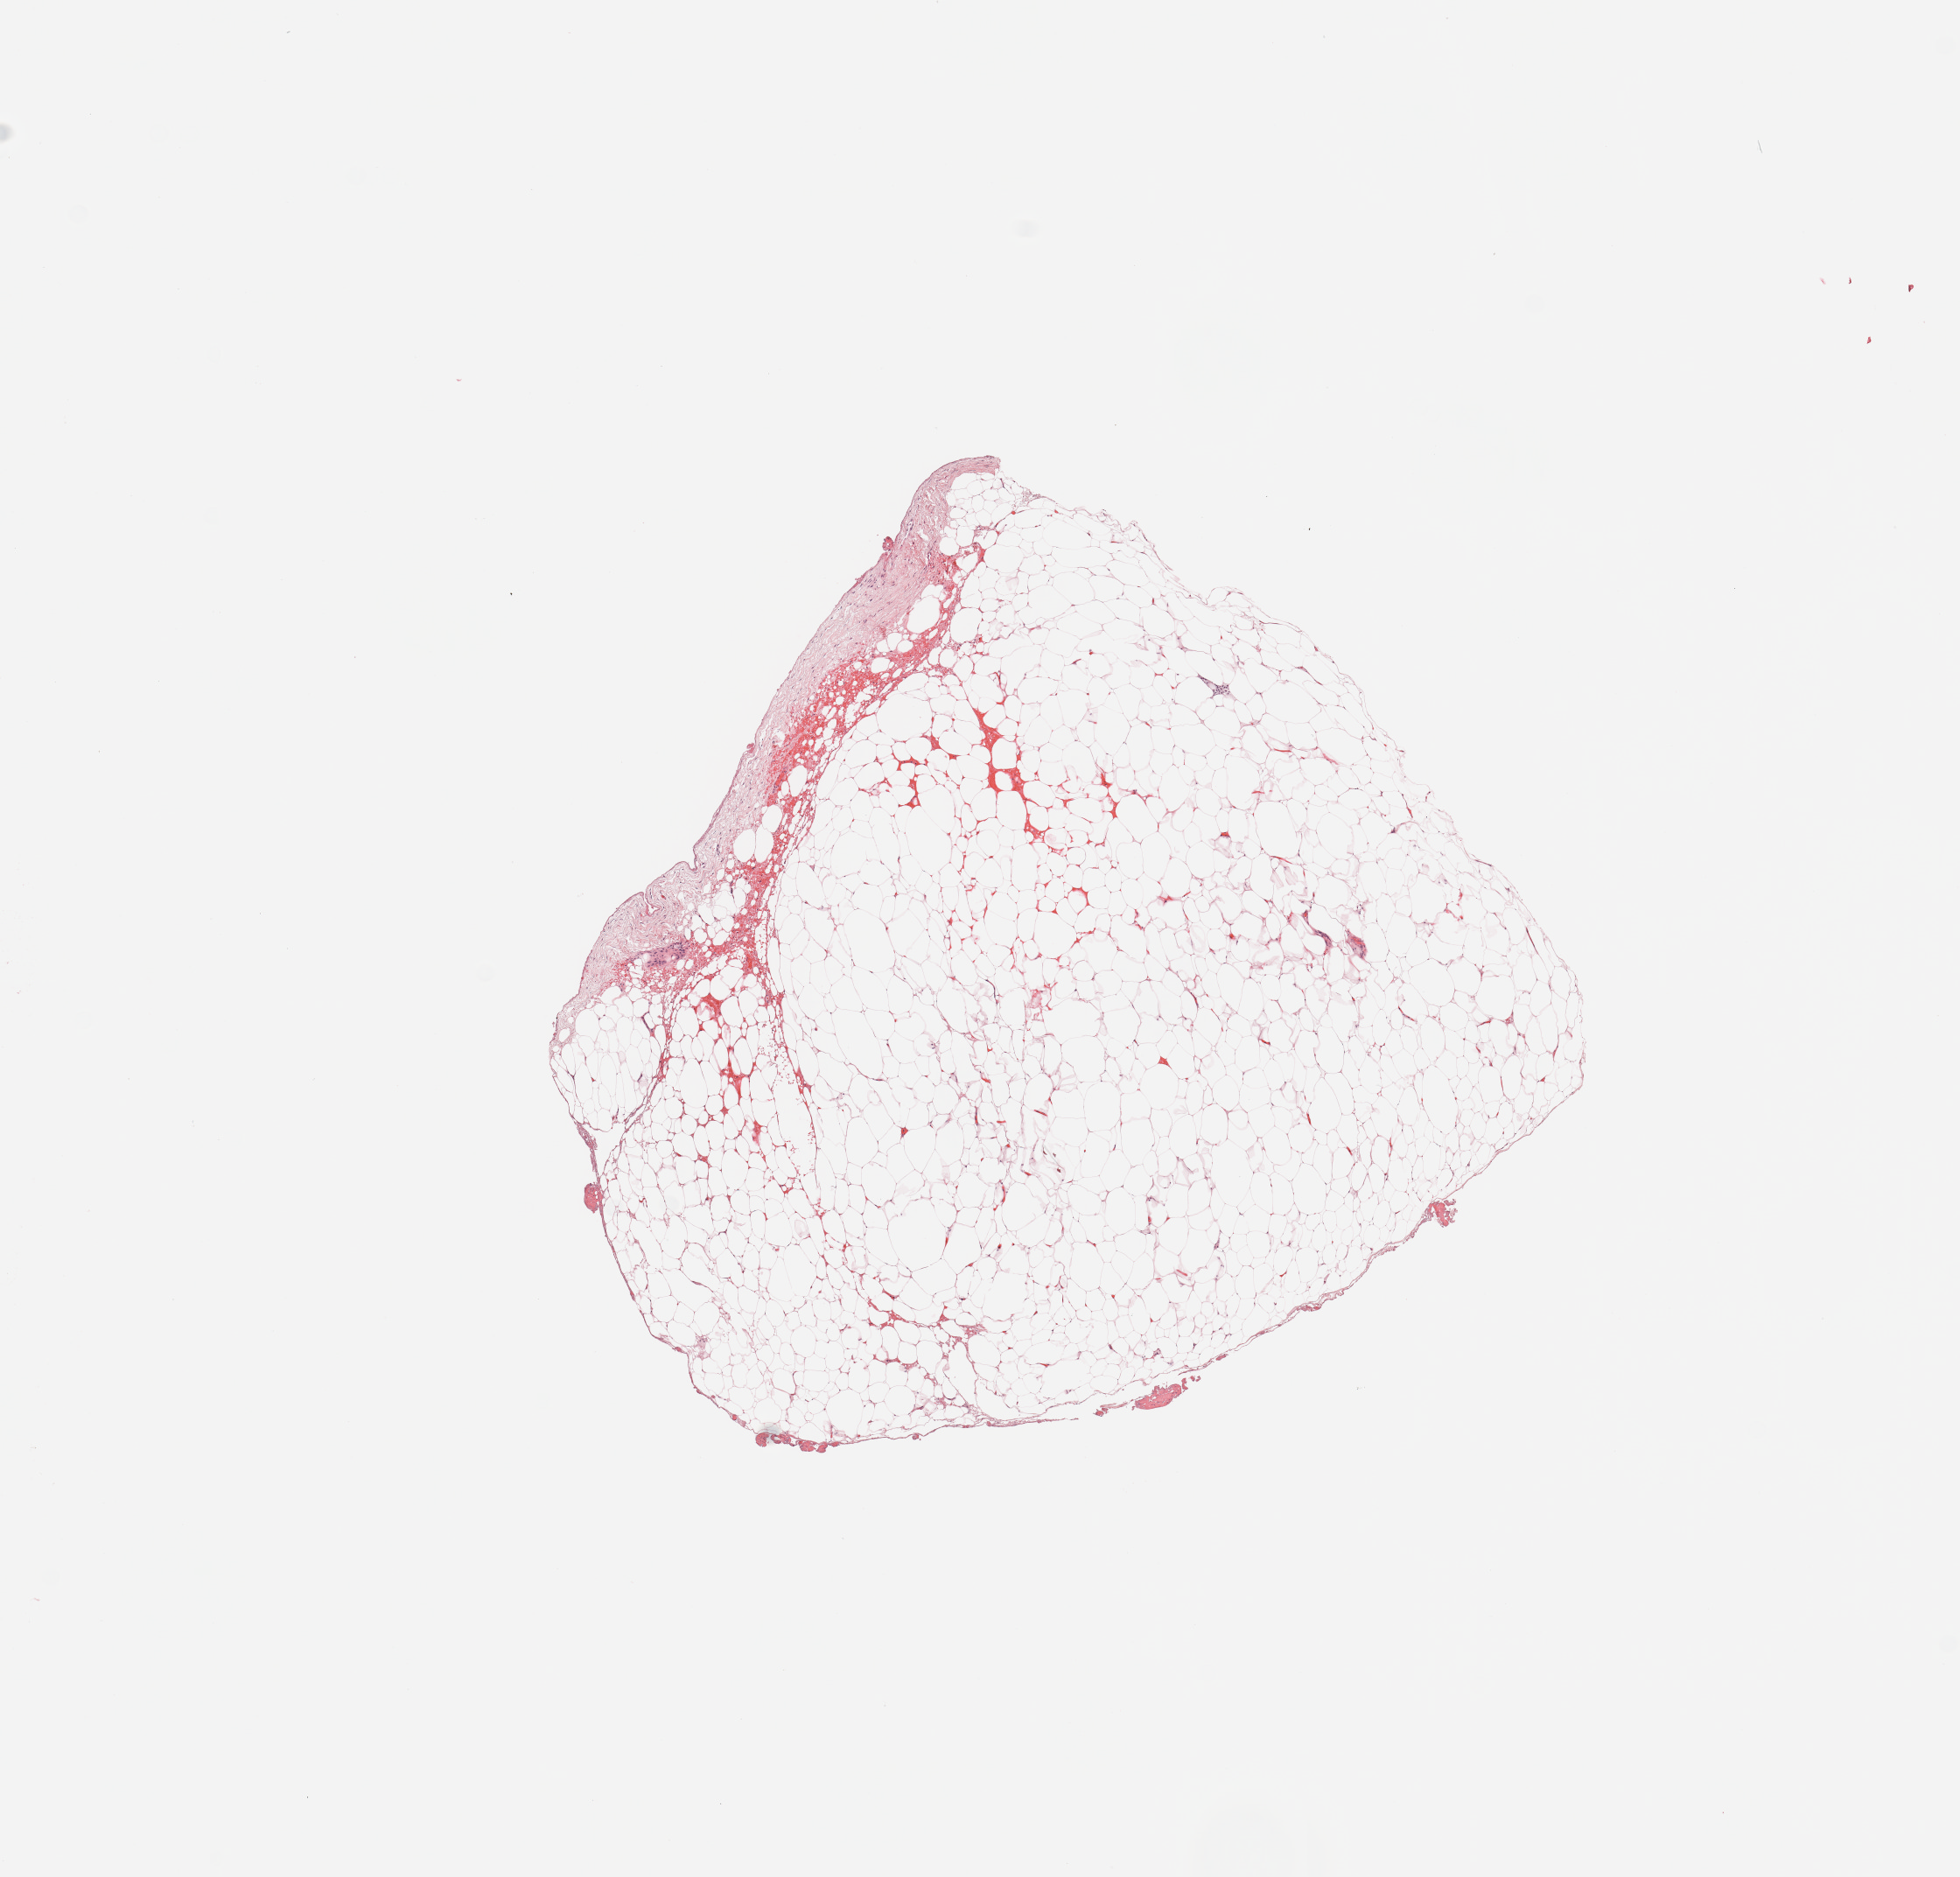
Whole-slide histology image, H&E, low-resolution overview of the scanned area, about 8.9 x 8.5 mm. Normal (non-tumour) tissue sample, kidney. Patient: female, age 67 years.
- this section: normal (non-tumour) tissue from the same patient
- patient diagnosis: Renal cell carcinoma, NOS